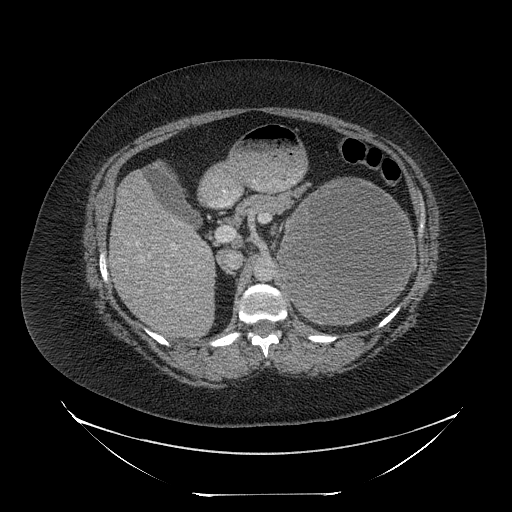
Contrast-enhanced abdominal CT, one axial slice; position 144 of 205 along the scan axis; 120 kVp; intravenous contrast given; soft-tissue window (W 400 / L 40 HU); 512 × 512 image matrix, field of view 500 × 500 mm. Patient: female, 53 years. From the clinical record (not read from this slice): diagnosis: adrenocortical carcinoma; tumour side: left adrenal.
Structures marked on this image (semi-automatic segmentation, software-assisted and operator-edited):
- mass: bounding box <280,179,413,321> (left, top, right, bottom; pixels)